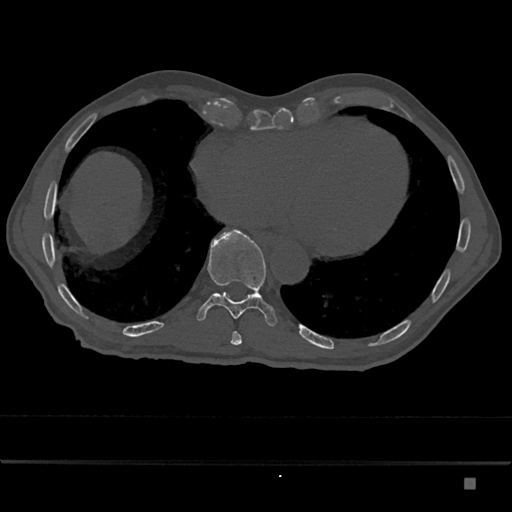
CT including the spine, one axial slice. Position 743 of 797 along the scan axis. Reconstruction kernel Br40s/3. Bone window (W 1800 / L 400 HU). 0.5 mm slice thickness. 512 × 512 image matrix, field of view 390 × 390 mm. Patient: male, 72 years. Case-level facts recorded for this patient, not image findings: primary cancer: prostate.
Outlined on this slice (semi-automatic segmentation, software-assisted and operator-edited):
- T10 vertebra: bounding box (x1, y1, x2, y2) in pixels: (197, 229, 277, 326)
- T9 vertebra: (231, 332, 242, 345)